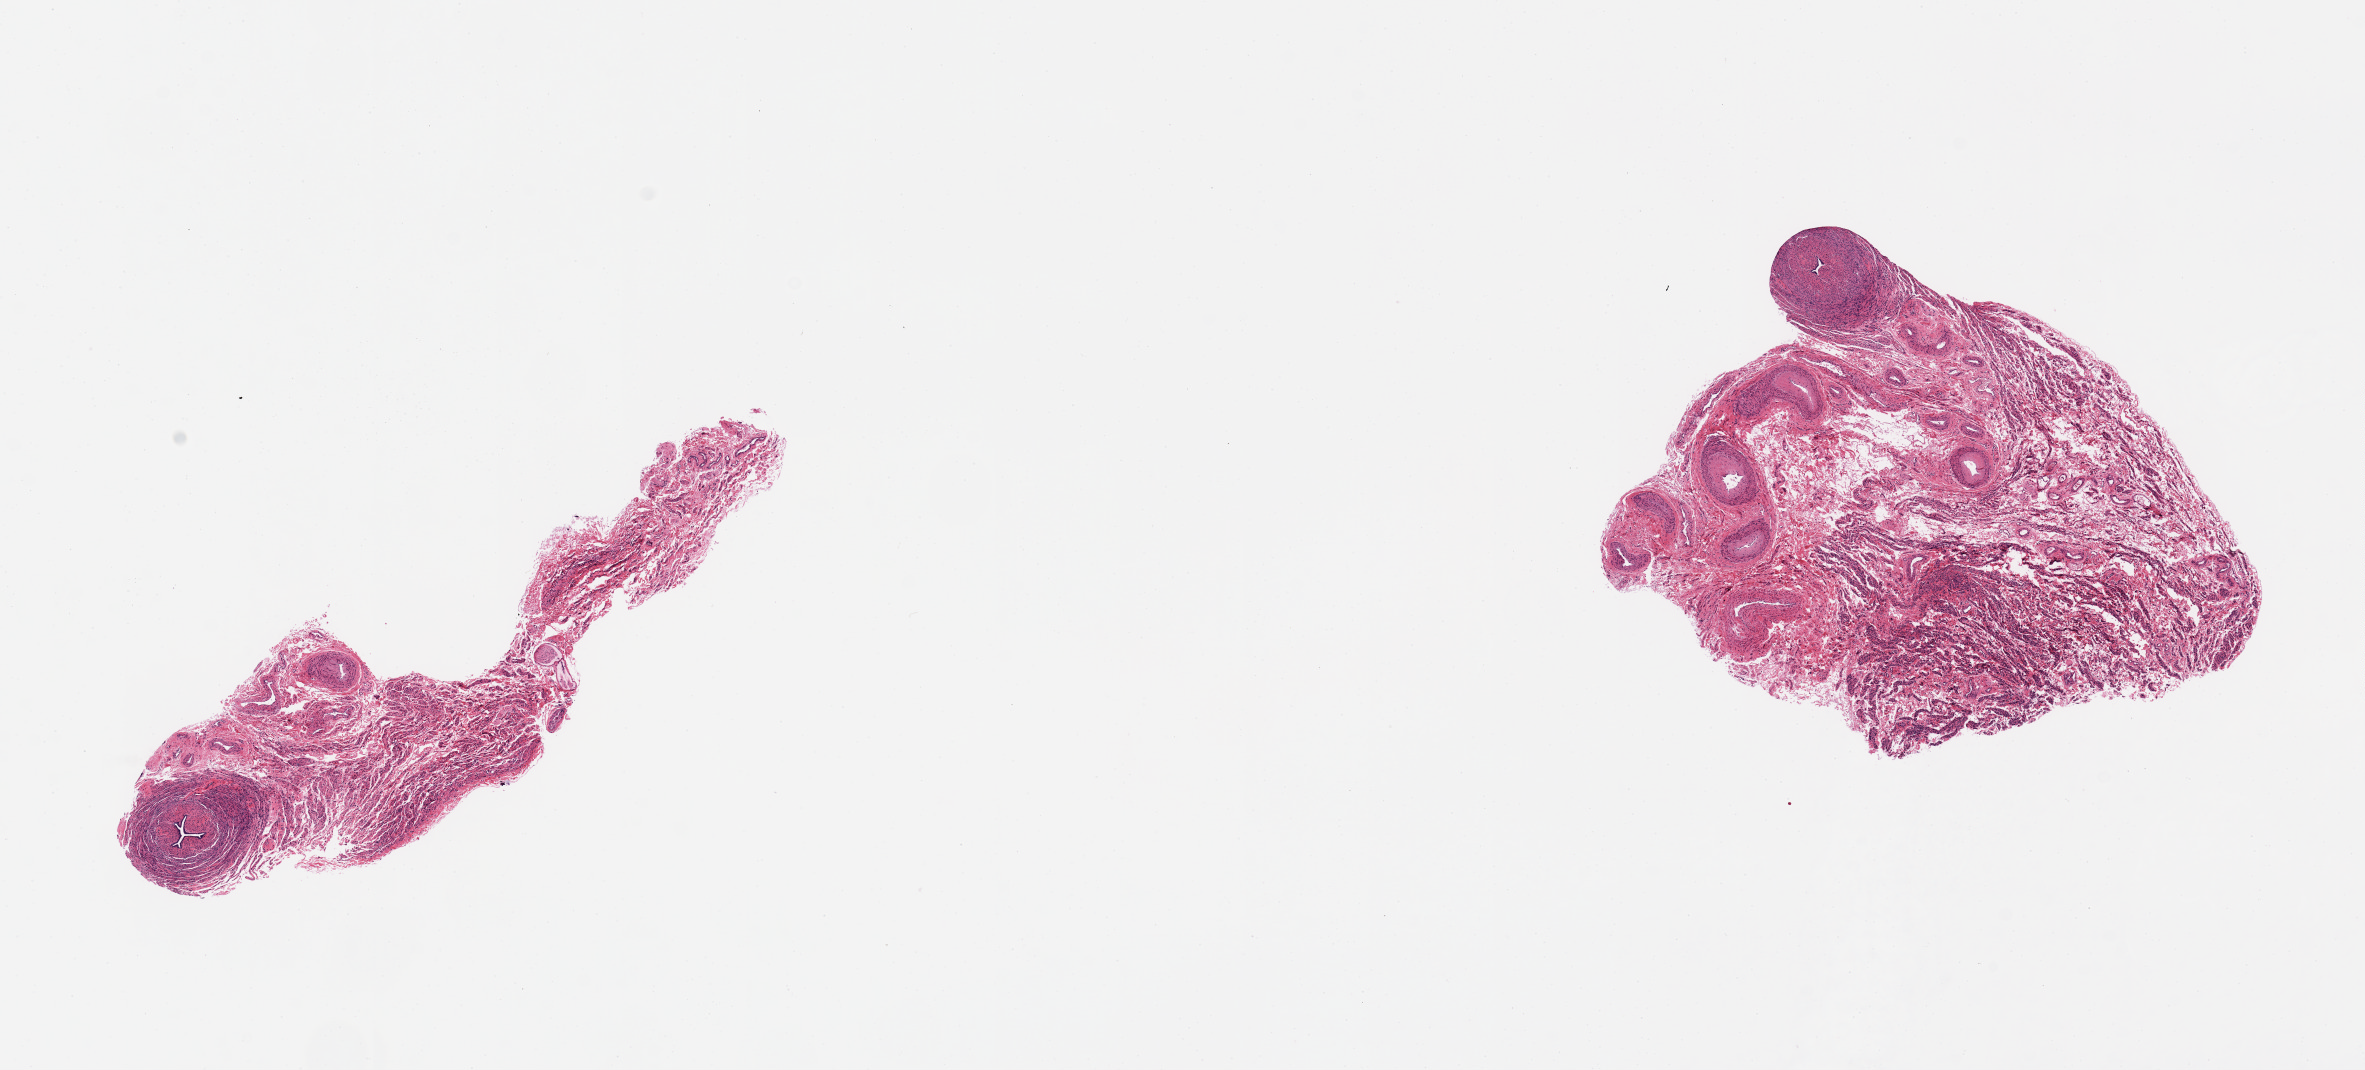
Digitized H&E-stained section, whole scanned area (about 18.7 x 8.5 mm) shown as a low-resolution overview, PAXgene-fixed, paraffin-embedded tissue, section of fallopian tube (target tissue), donor tissue sample. Donor: female.
• pathologist's review note for this sample: Very little tube present